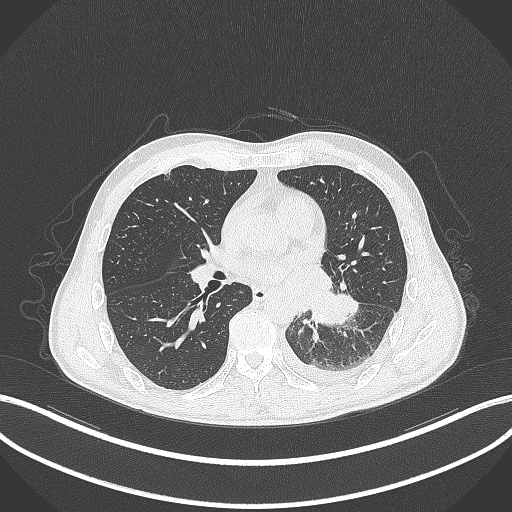
Chest CT, one axial slice. Position 156 of 295 along the scan axis. Reconstruction kernel B70f. 120 kVp. Lung window (W 1500 / L -600 HU). 1 mm slice thickness. 512 × 512 image matrix, field of view 400 × 400 mm. Patient: male, 47 years. From the clinical record (not read from this slice): clinical TNM (as recorded): T3 N1 M1c; histopathological grade: G3.
Annotated regions visible in this slice (bounding box drawn by a radiologist):
- lung tumour (recorded histology: small cell carcinoma): bounding box <306,286,363,329> (left, top, right, bottom; pixels)